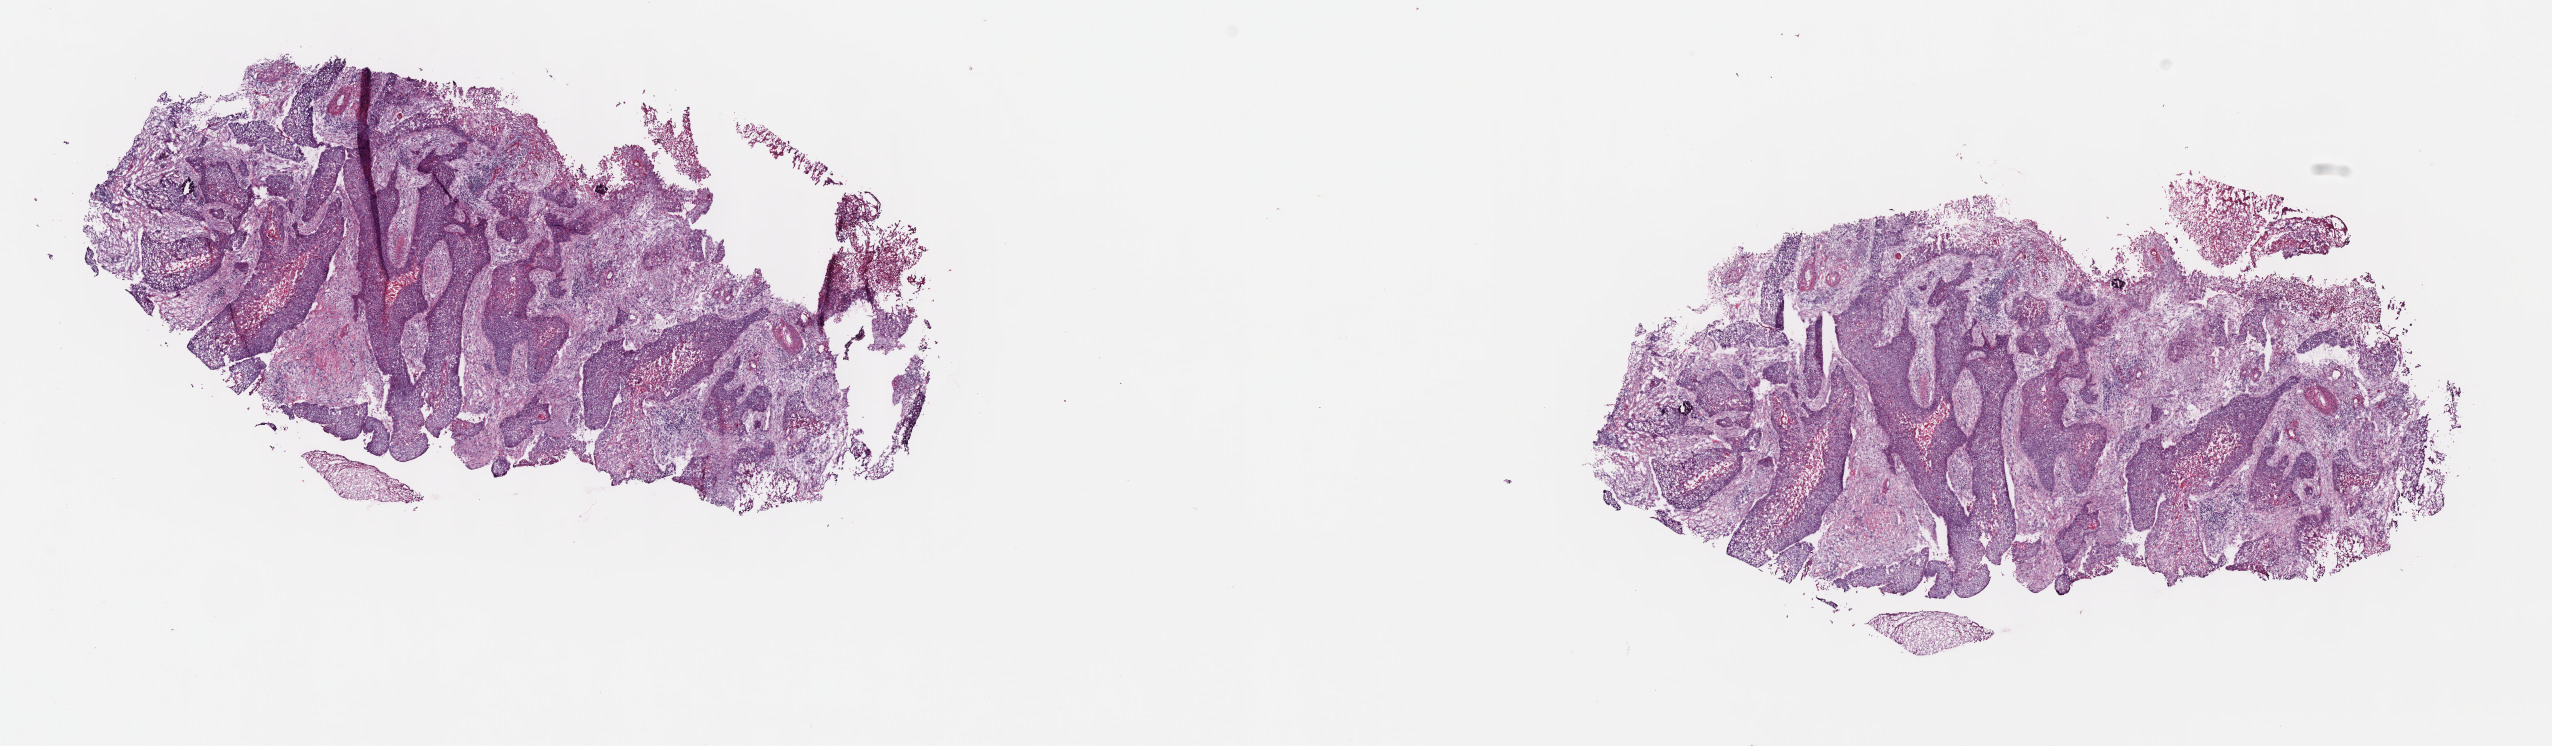
Digitized H&E-stained tissue section (whole slide) — a low-resolution overview of the entire scanned area, about 20.6 x 6.0 mm. Frozen section from the top of the tissue portion. Cervix, primary tumour sample. Patient: female, age at initial diagnosis 58 years. Histologic grade: G2 (moderately differentiated). Pathologist review of this section (percent, as recorded): tumour cells 100%, tumour nuclei 60%, normal cells 0%, stromal cells 0%, necrosis 0%. Inflammatory infiltration, as recorded: lymphocyte infiltration 5%, monocyte infiltration 0%, neutrophil infiltration 0%.
Histologic diagnosis: Squamous cell carcinoma, NOS (cervix uteri). FIGO stage: IVA.